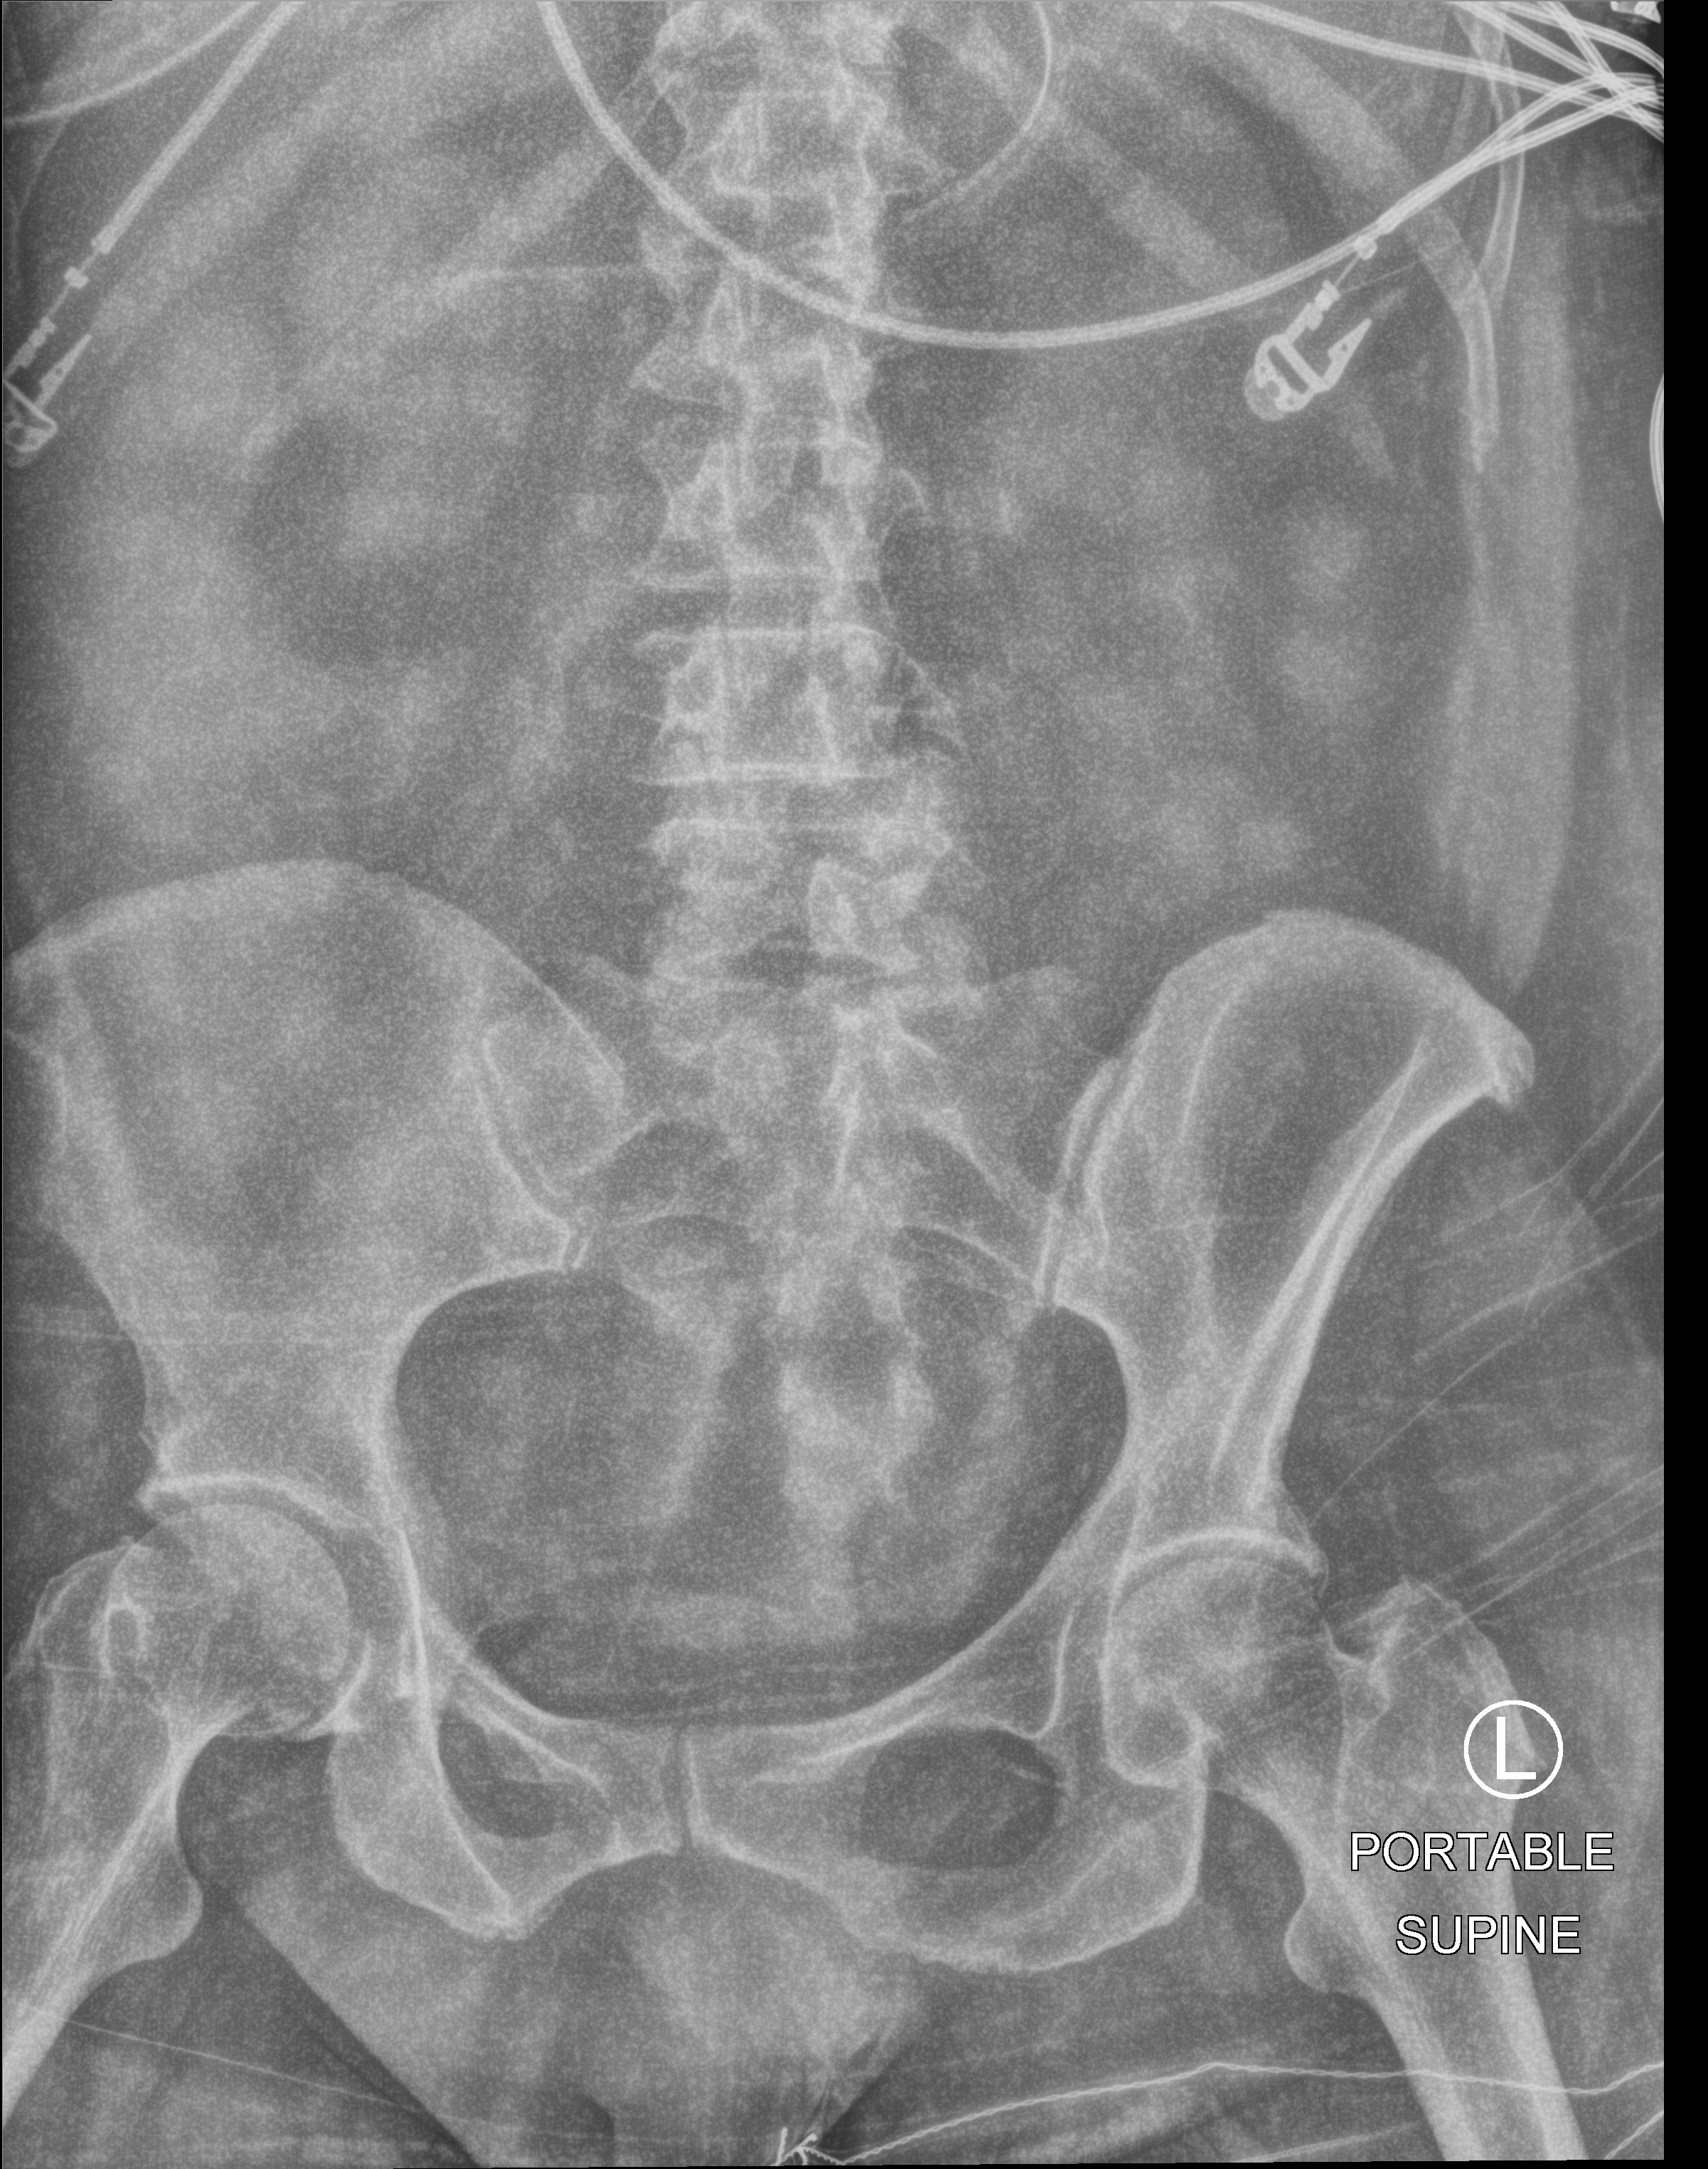
Bedside abdomen radiograph (computed radiography); anteroposterior (AP) projection. Patient hospitalised with COVID-19; female, aged 60–74 years.
From the hospital-stay record, not from the radiograph (when in the stay this image was taken is not recorded): smoking status (admission record): former.